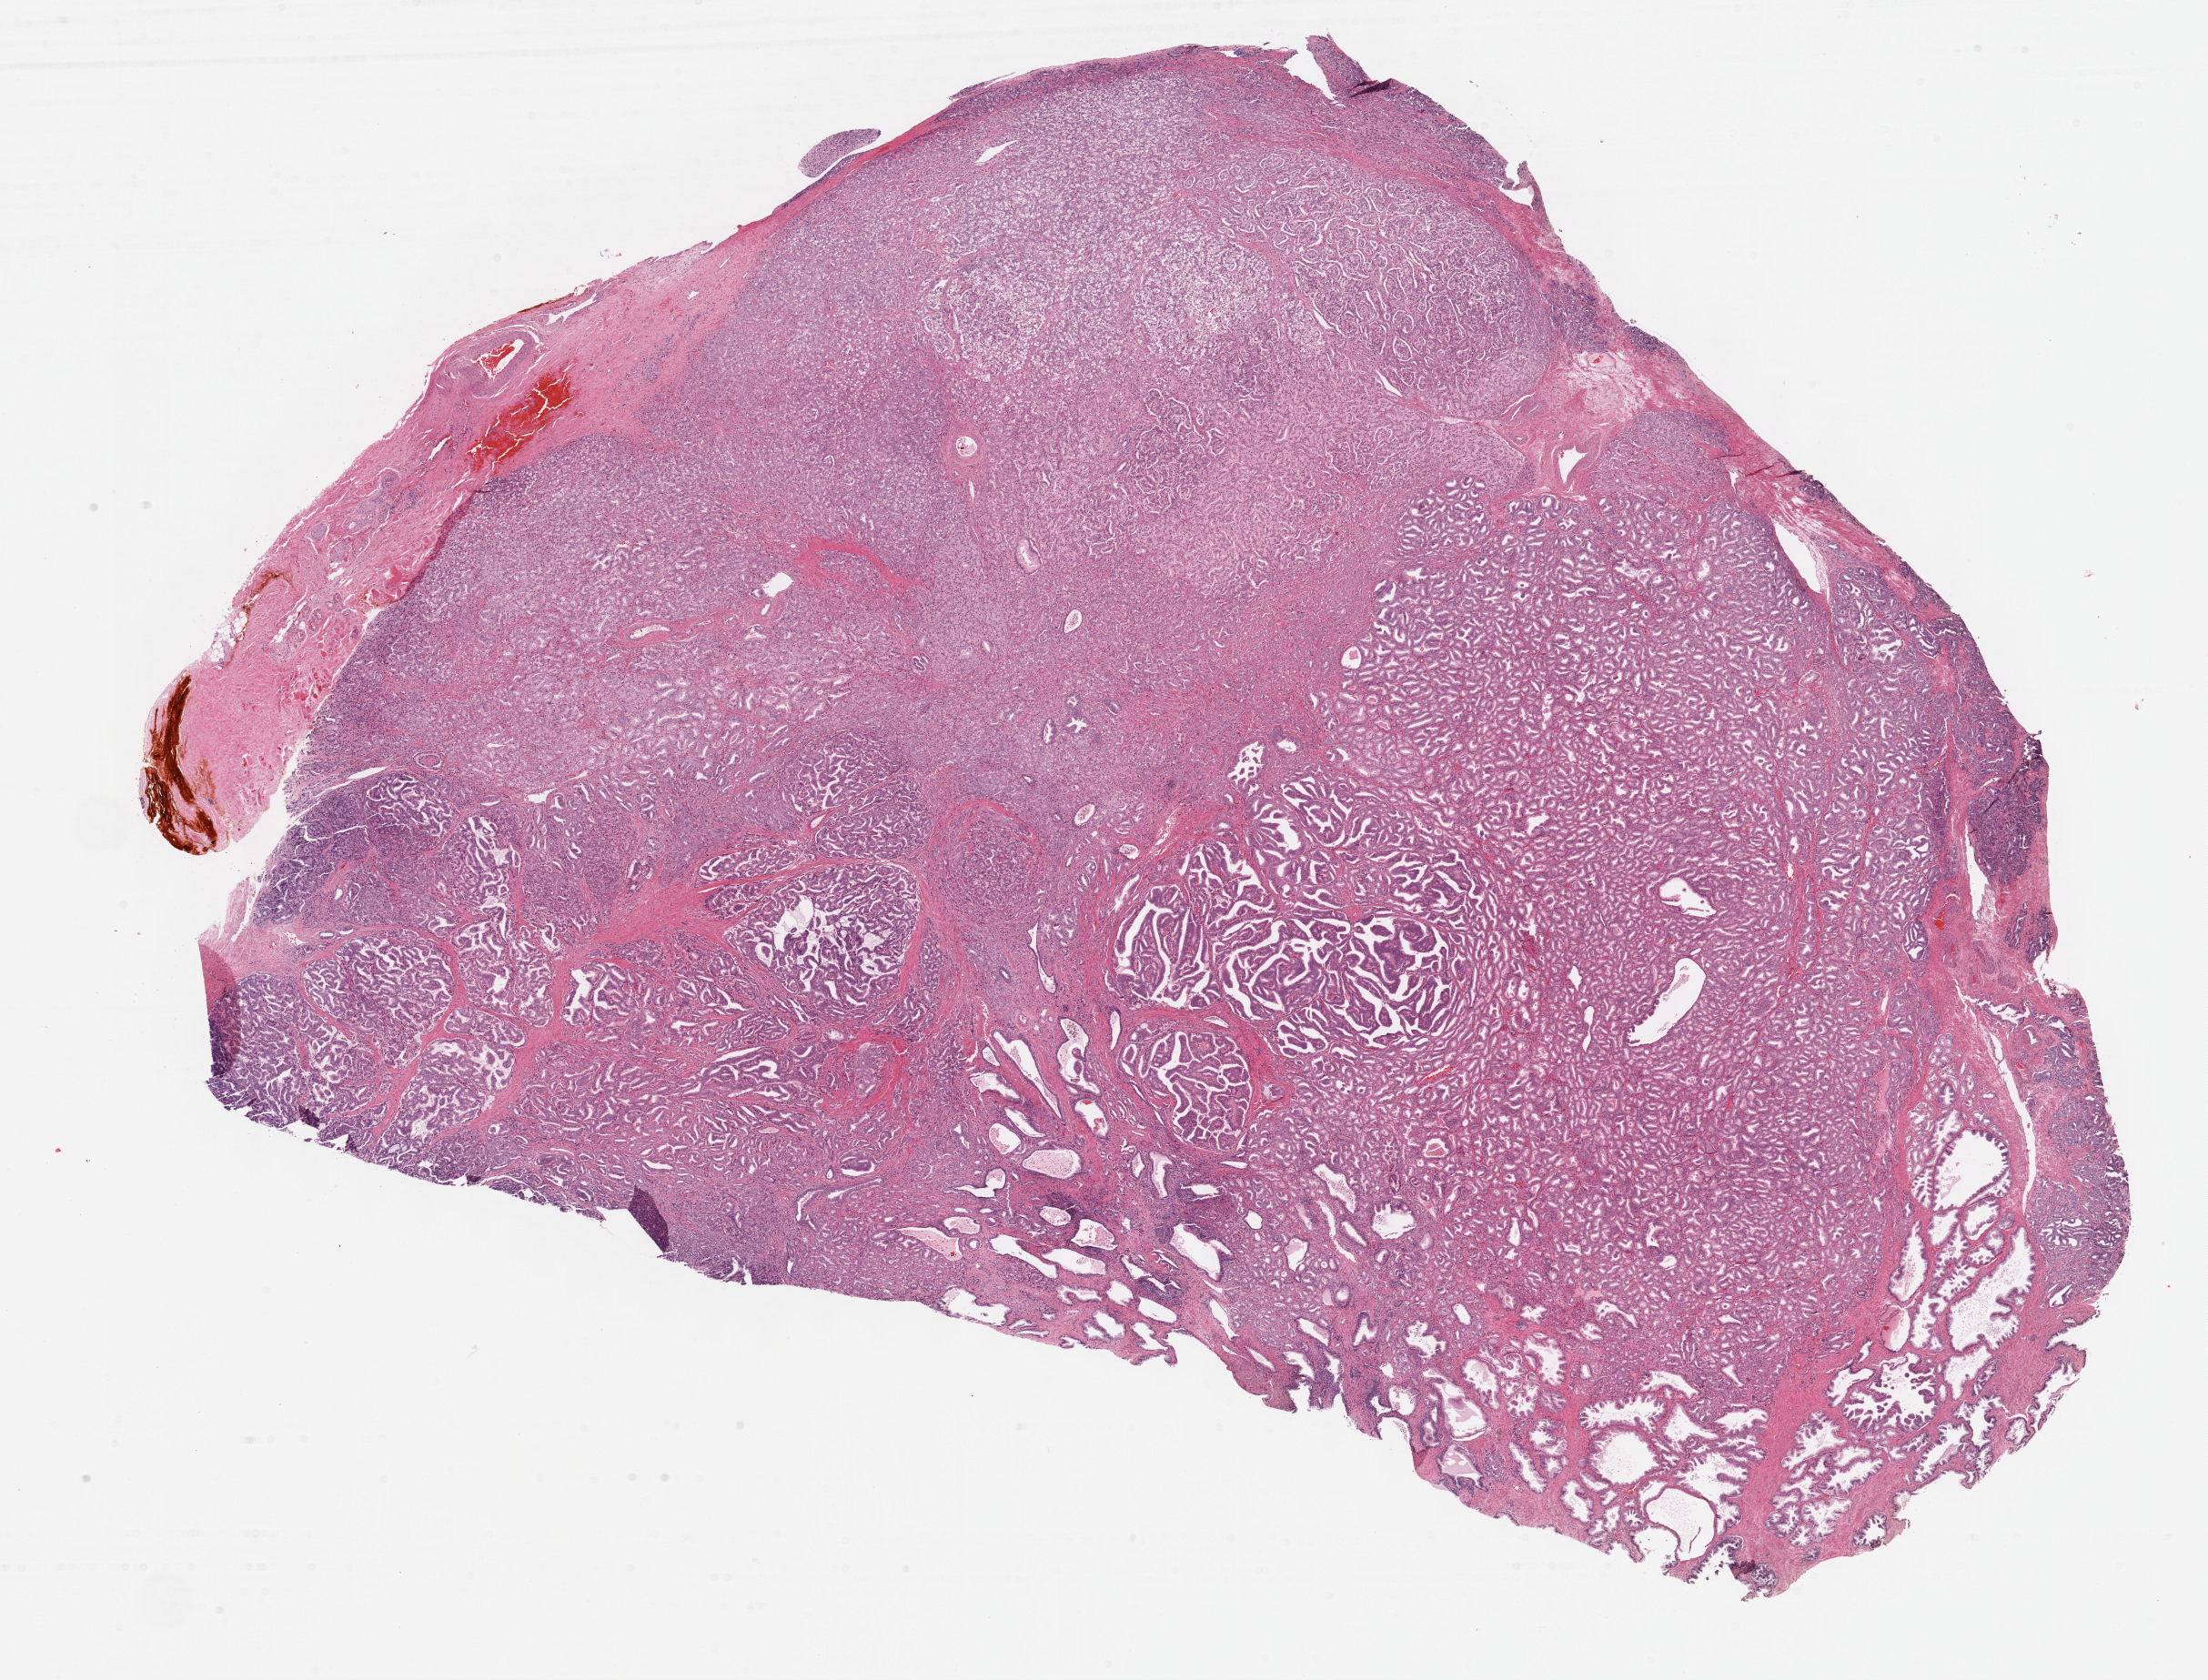
H&E whole-slide image — shown as a low-resolution overview of the whole scanned area (about 19.6 x 14.9 mm, from a 40x scan), formalin-fixed paraffin-embedded (FFPE) diagnostic section, prostate, primary tumour sample. Male patient; age at initial diagnosis 62 years. Gleason score: 7 (4+3).
Histologic diagnosis: Adenocarcinoma, NOS (prostate gland). Laterality: bilateral.